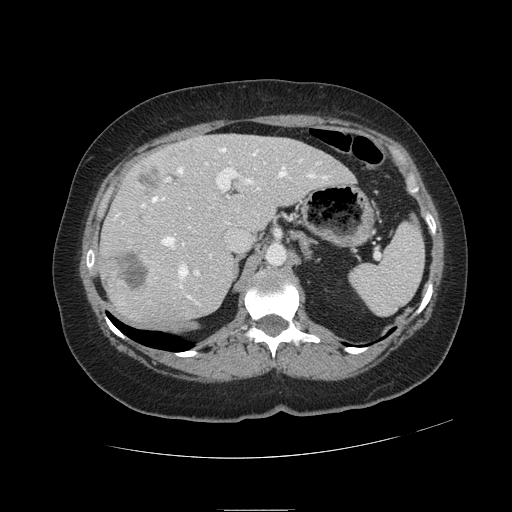
Contrast-enhanced abdominal CT, one axial slice. Slice 72 of 121 in the series (ordered by position). Intravenous contrast given. Soft-tissue window (W 400 / L 40 HU). 2.5 mm slice thickness. 512 × 512 image matrix. Female patient, age 52 years. From the clinical record (not read from this slice): diagnosis: colorectal cancer liver metastases, imaged before liver resection; multiple liver metastases: yes; largest metastasis: 6.3 cm.
Structures marked on this image (outlined manually by an expert reader):
- hepatic veins: bounding box [x1, y1, x2, y2] px = [116, 148, 328, 298]
- liver: [101, 135, 353, 323]
- planned liver remnant (the part of the liver to remain after resection): [167, 135, 352, 229]
- portal vein (with intrahepatic branches): [122, 162, 265, 276]
- liver metastasis: [139, 167, 159, 189]
- liver metastasis: [121, 255, 148, 289]